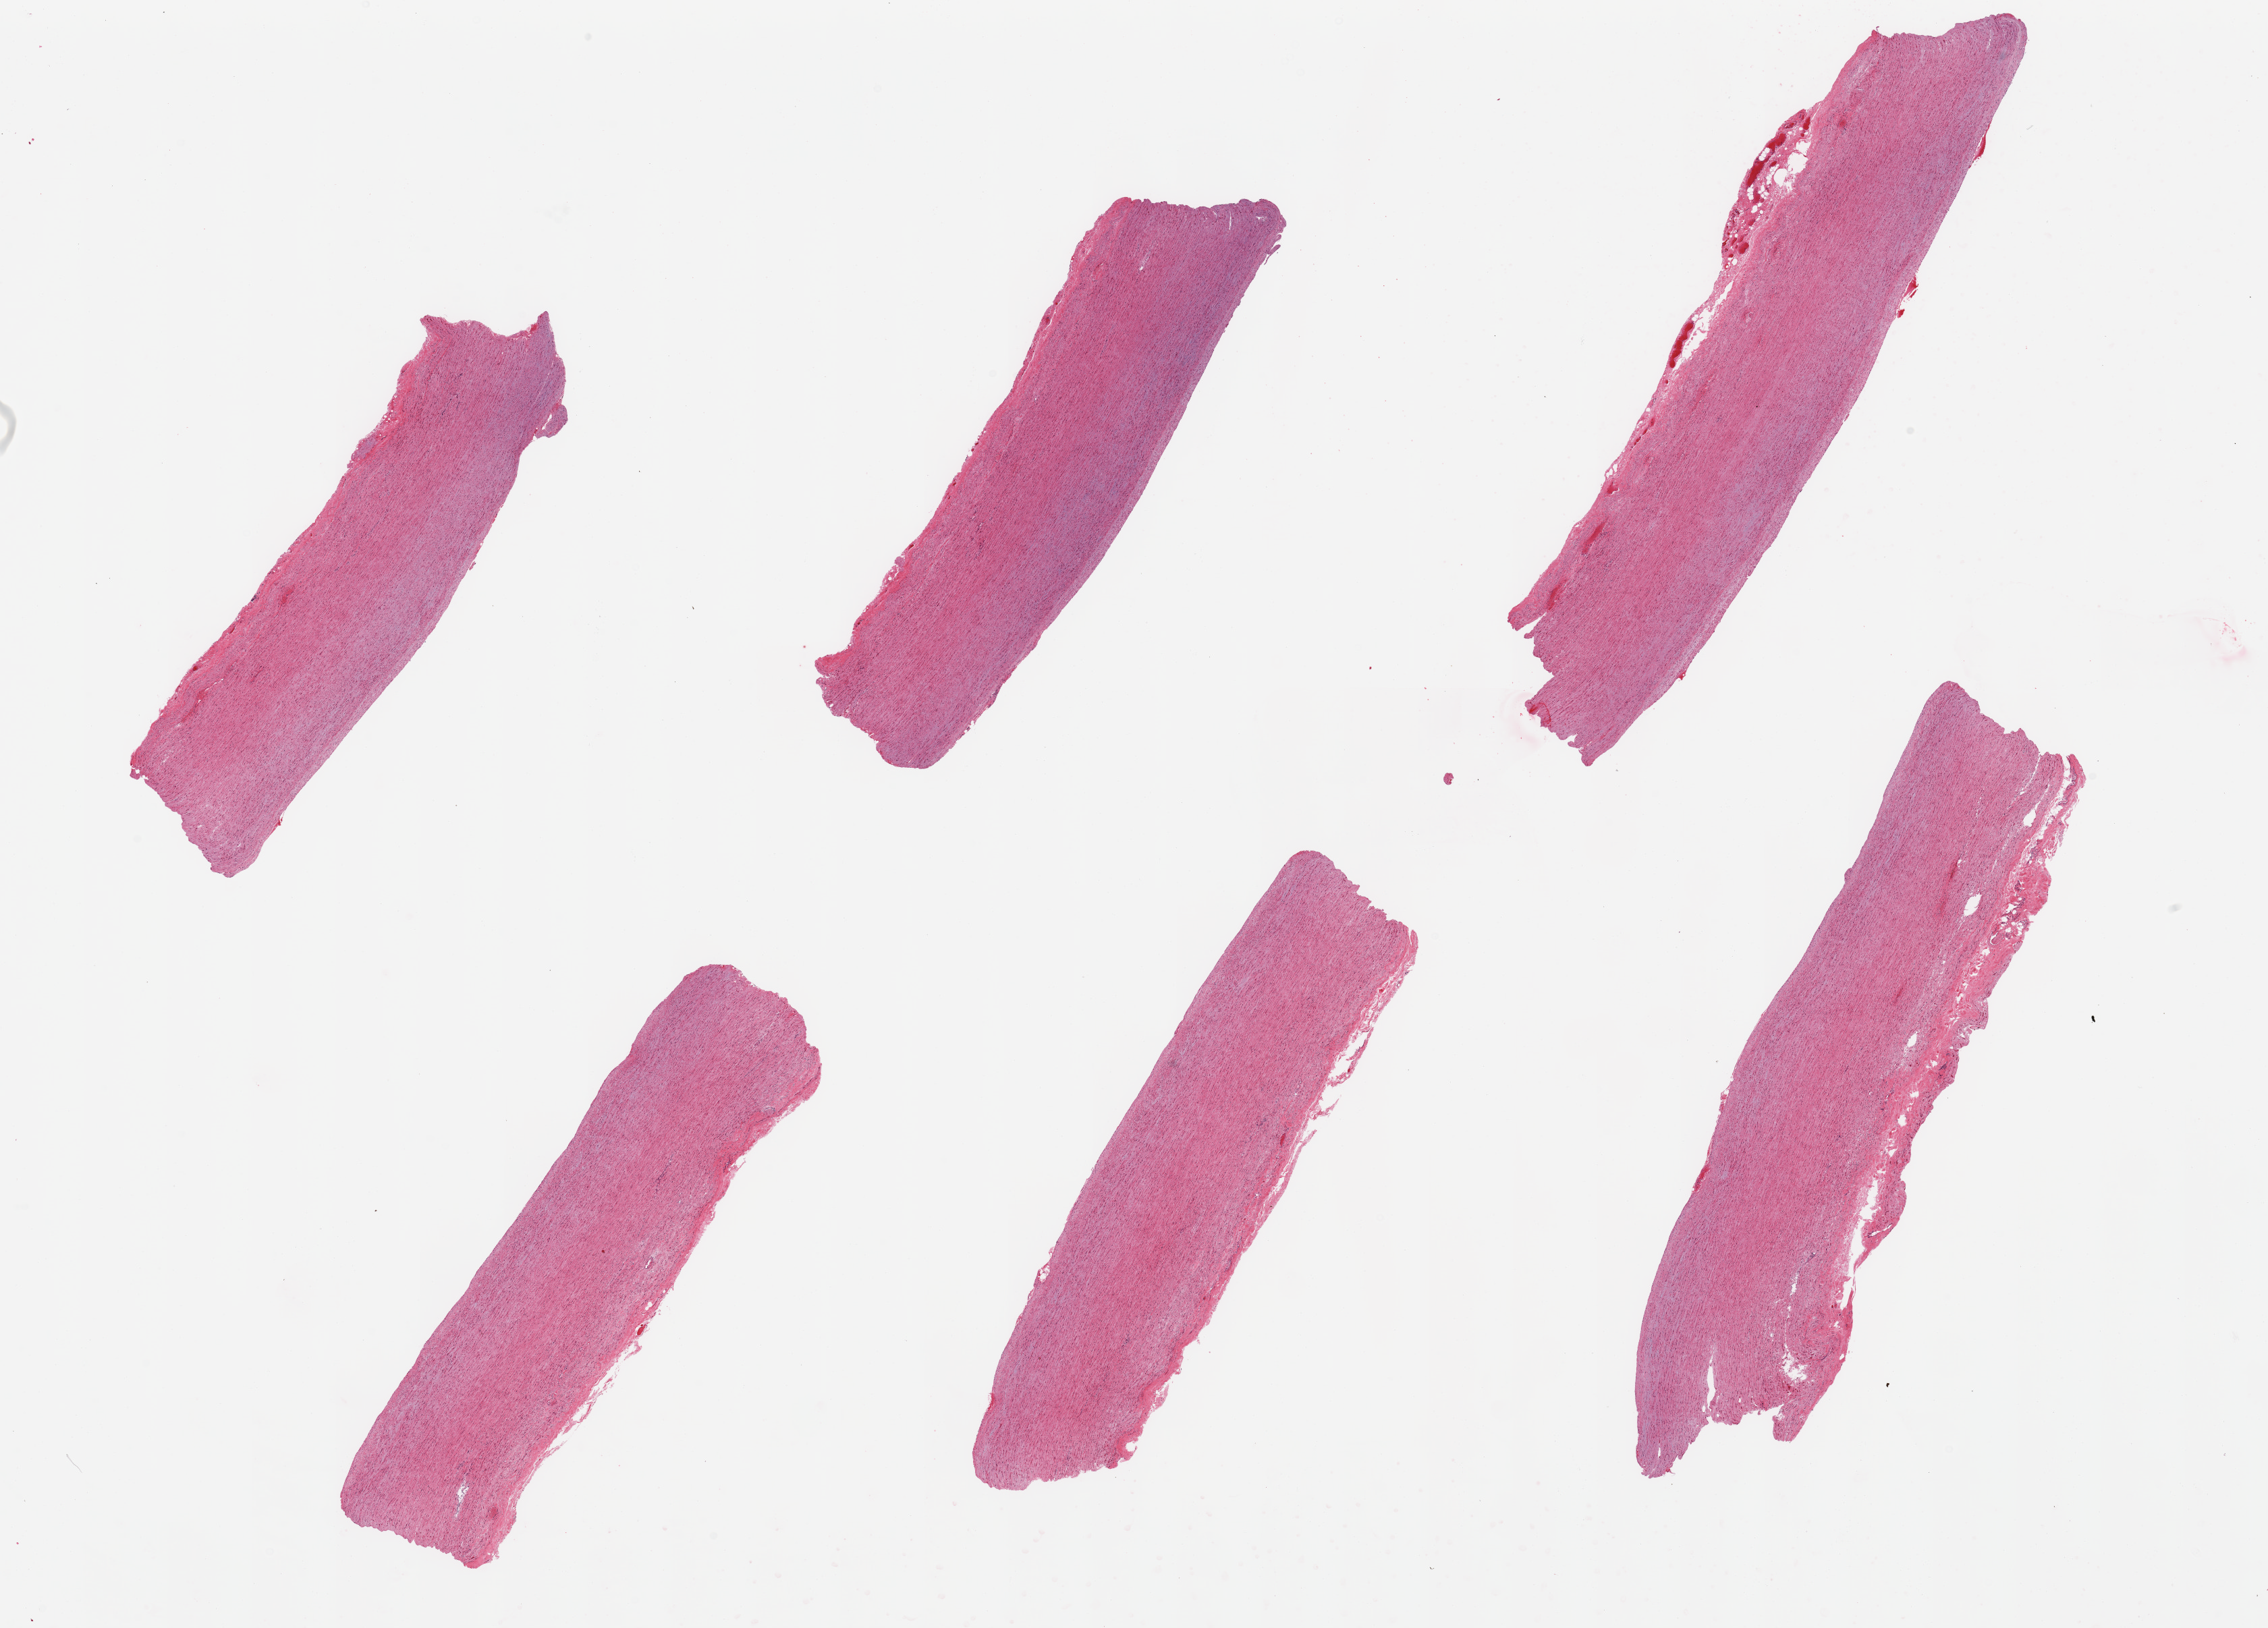
Hematoxylin and eosin (H&E) whole-slide image, whole scanned area (about 26.6 x 19.1 mm, from a 20x scan) shown as a low-resolution overview; PAXgene-fixed, paraffin-embedded tissue; sampled site (target tissue): aorta; tissue donor sample. Donor: male.
Reviewer comment on this tissue sample: 6 pieces, minimal atherosis.